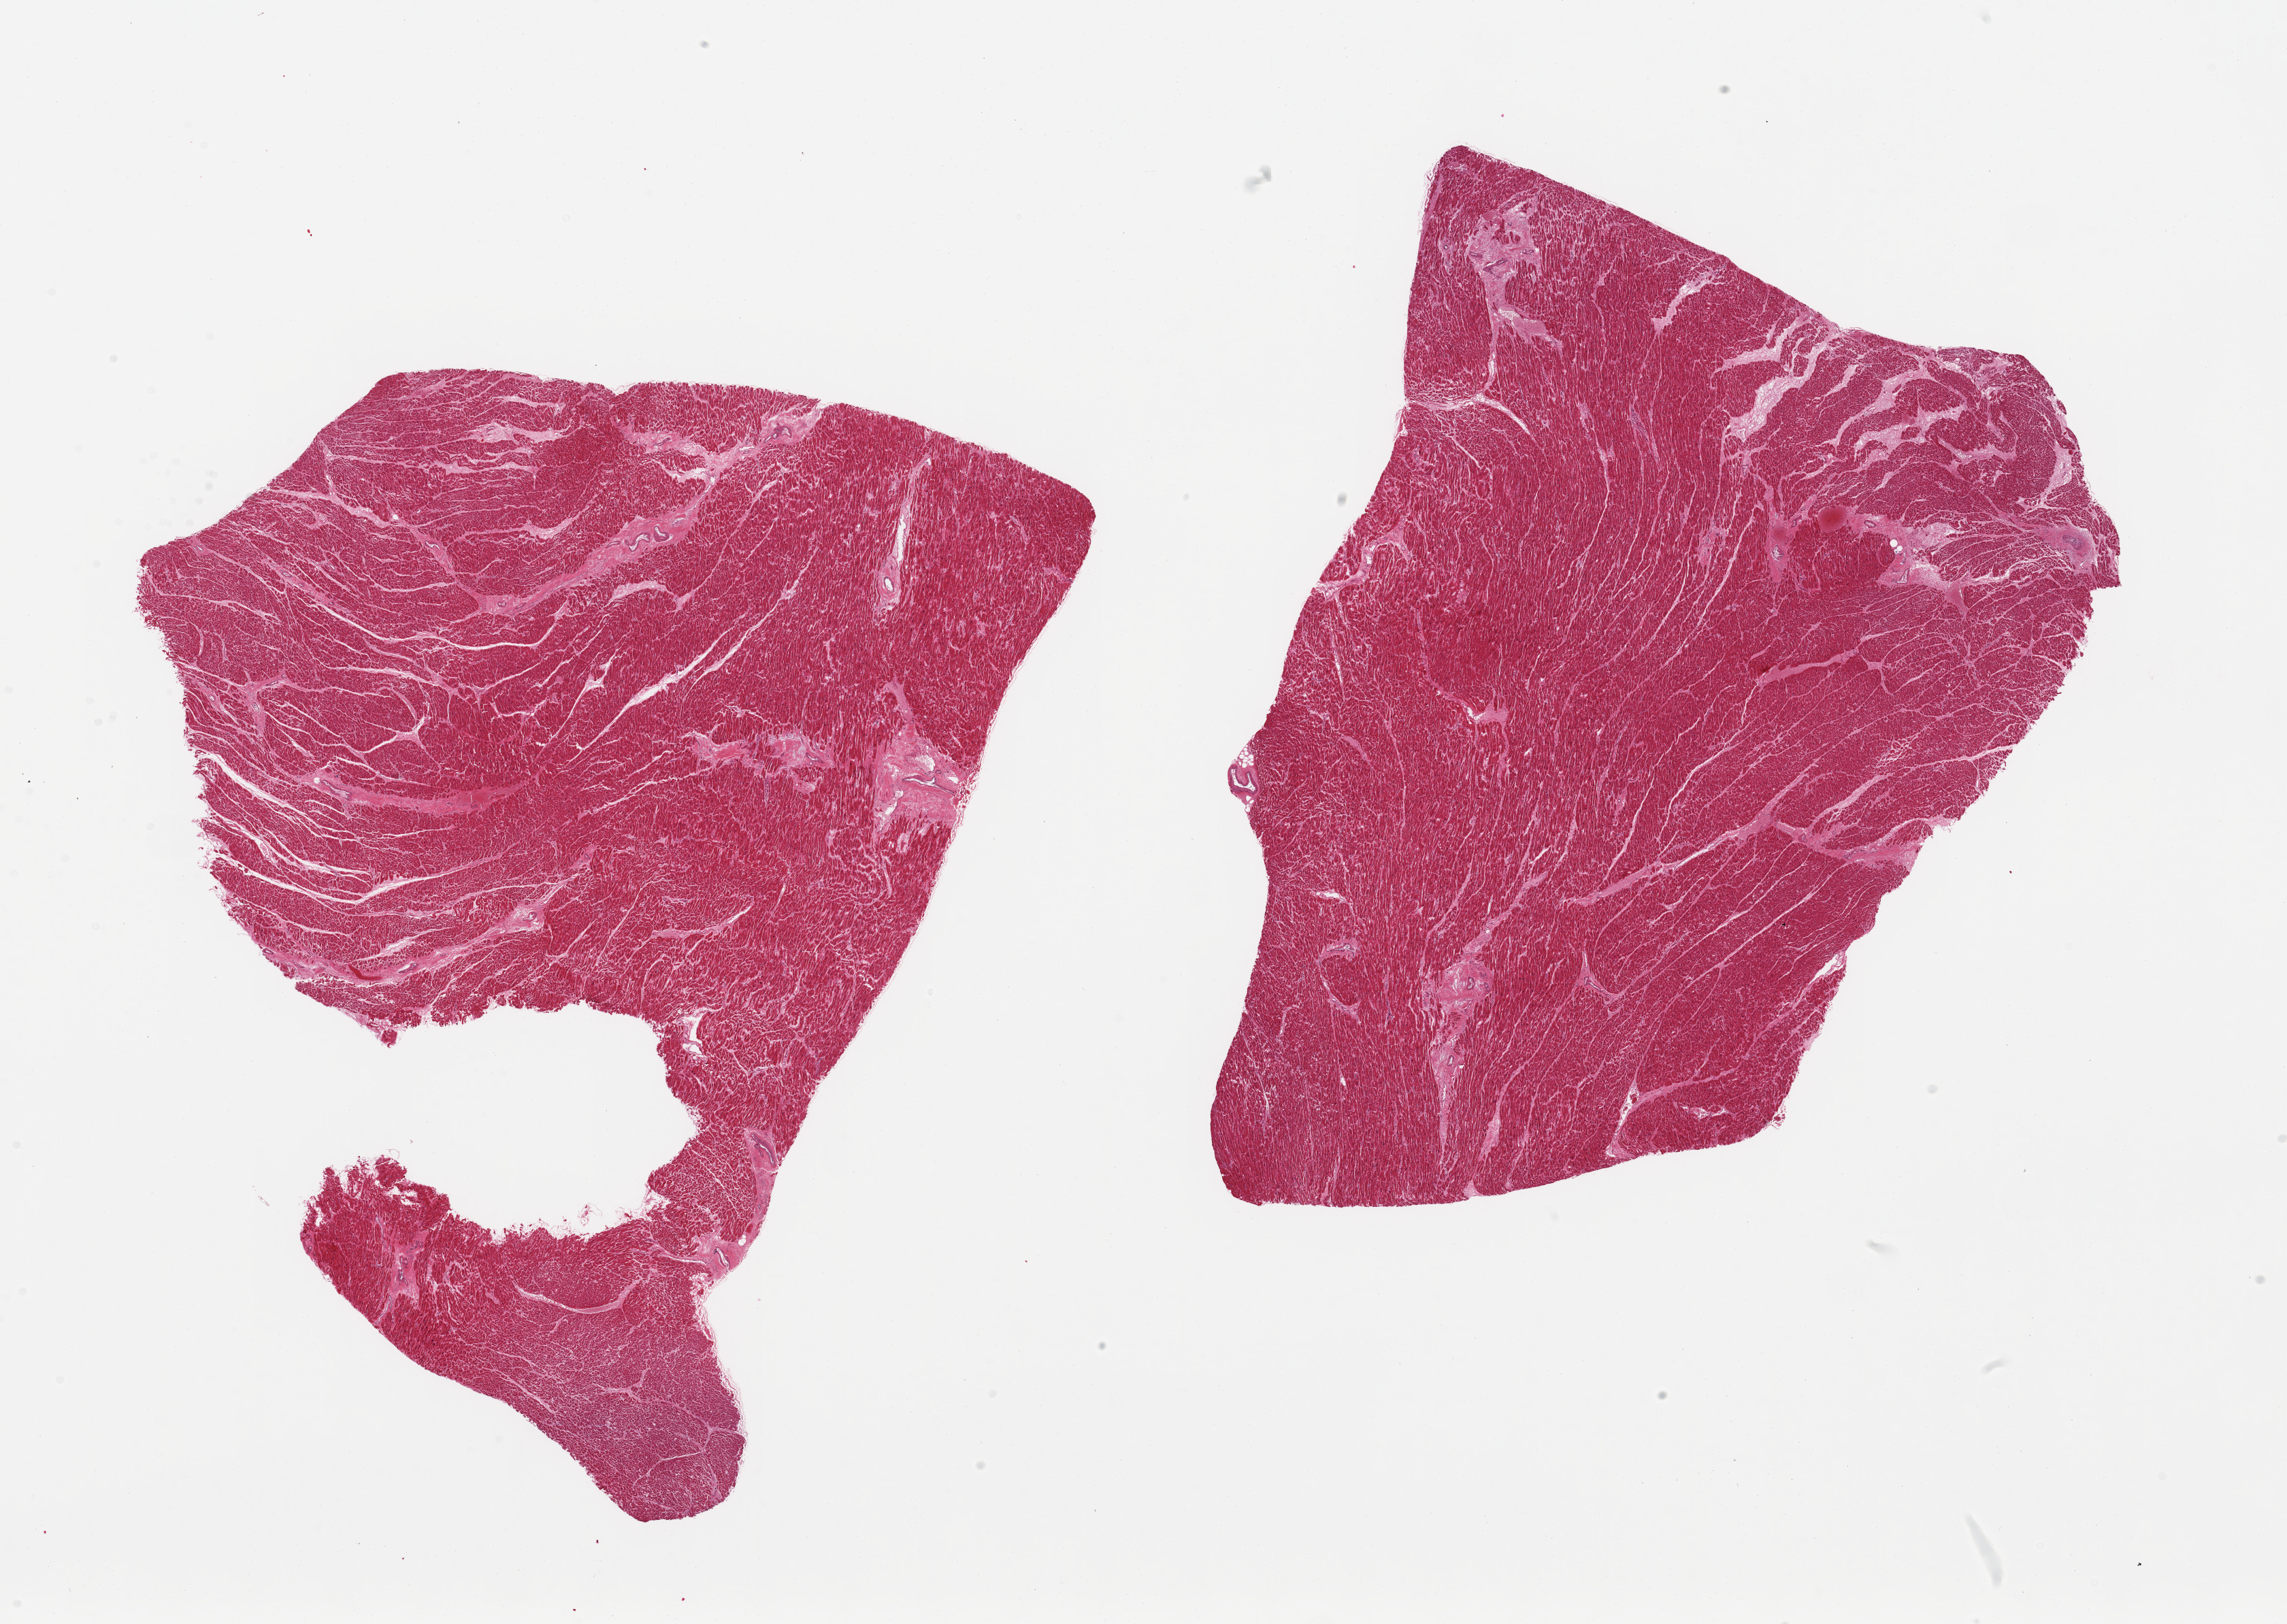
Haematoxylin and eosin whole-slide image — a low-resolution overview of the entire scanned area, about 26.6 x 18.9 mm (from a 20x scan); PAXgene-fixed, paraffin-embedded tissue; sampled site (target tissue): heart; tissue donor sample. Male donor.
Review note (as recorded): 2 pieces, mild/moderate interstitial fibrosis/chronic ischemic changes.